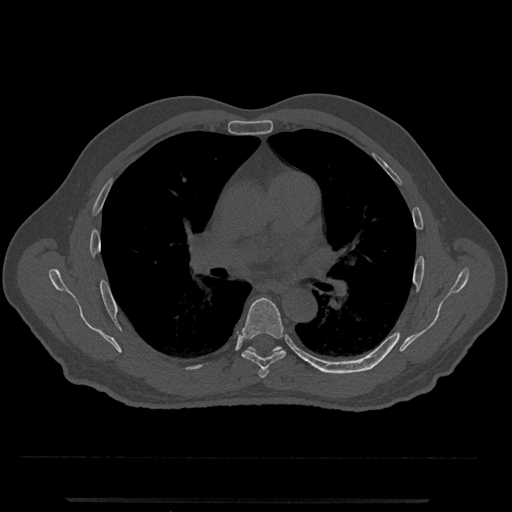
CT including the spine, one axial slice. Slice 730 of 797 in the series (ordered by position). Reconstruction kernel Br40s/3. Bone window (W 1800 / L 400 HU). 0.5 mm slice thickness. 512 × 512 image matrix, field of view 419 × 419 mm. Patient: male, 63 years. From the clinical record (not read from this slice): primary cancer: prostate.
Outlined on this slice (semi-automatic segmentation, software-assisted and operator-edited):
- T5 vertebra: bounding box [x1, y1, x2, y2] px = [259, 369, 269, 378]
- T6 vertebra: [241, 298, 286, 369]
- T7 vertebra: [247, 346, 327, 373]